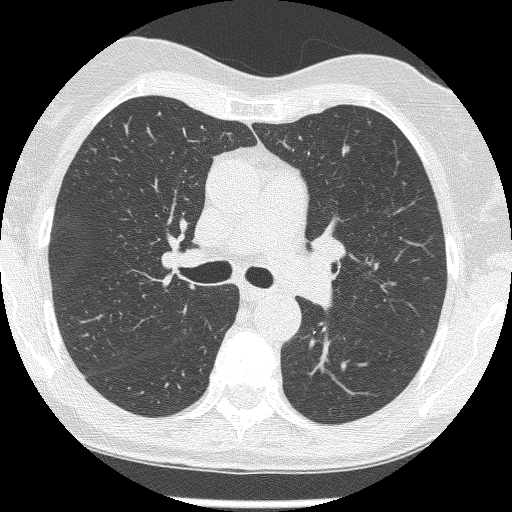
Chest CT (low-dose screening protocol), one axial image. Second screening round (one year after baseline). Lung window (W 1500 / L -600 HU). 120 kVp. Slice 173 of 250 in the series. Female, age 60 years at enrolment. Current smoker at enrolment.
Expert reader's lesion annotation, bounding box [x1, y1, x2, y2] px = [338, 139, 360, 163]. The screening reader recorded 2 non-calcified nodules or masses ≥4 mm on this exam (left upper lobe, left upper lobe); which of them this box marks is not recorded. Participant outcome: lung cancer diagnosed 428 days after this screen — adenocarcinoma, NOS, left upper lobe, moderately differentiated (G2), stage IA (AJCC 6th edition), 6 mm at pathology.